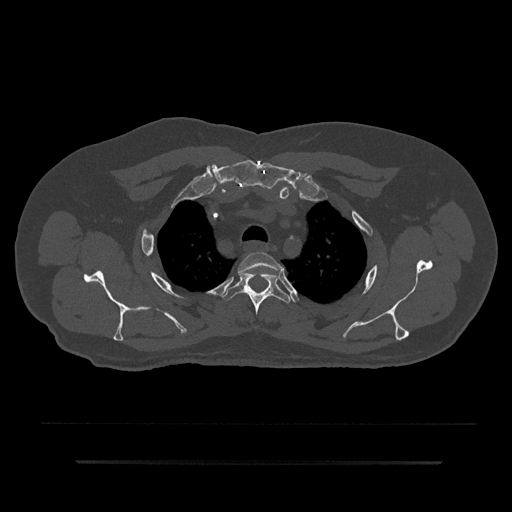
CT including the spine, one axial slice; position 669 of 797 along the scan axis; reconstruction kernel Br40s/3; 120 kVp; bone window (W 1800 / L 400 HU); 0.5 mm slice thickness; 512 × 512 image matrix, field of view 464 × 464 mm. Patient: male, 59 years. Case-level facts recorded for this patient, not image findings: primary cancer: bile ducts; vertebrae with lytic lesions (as recorded): T10.
Outlined on this slice (semi-automatically segmented with operator editing):
- T2 vertebra: bounding box <238,252,282,292> (left, top, right, bottom; pixels)
- T3 vertebra: <222,272,291,315>